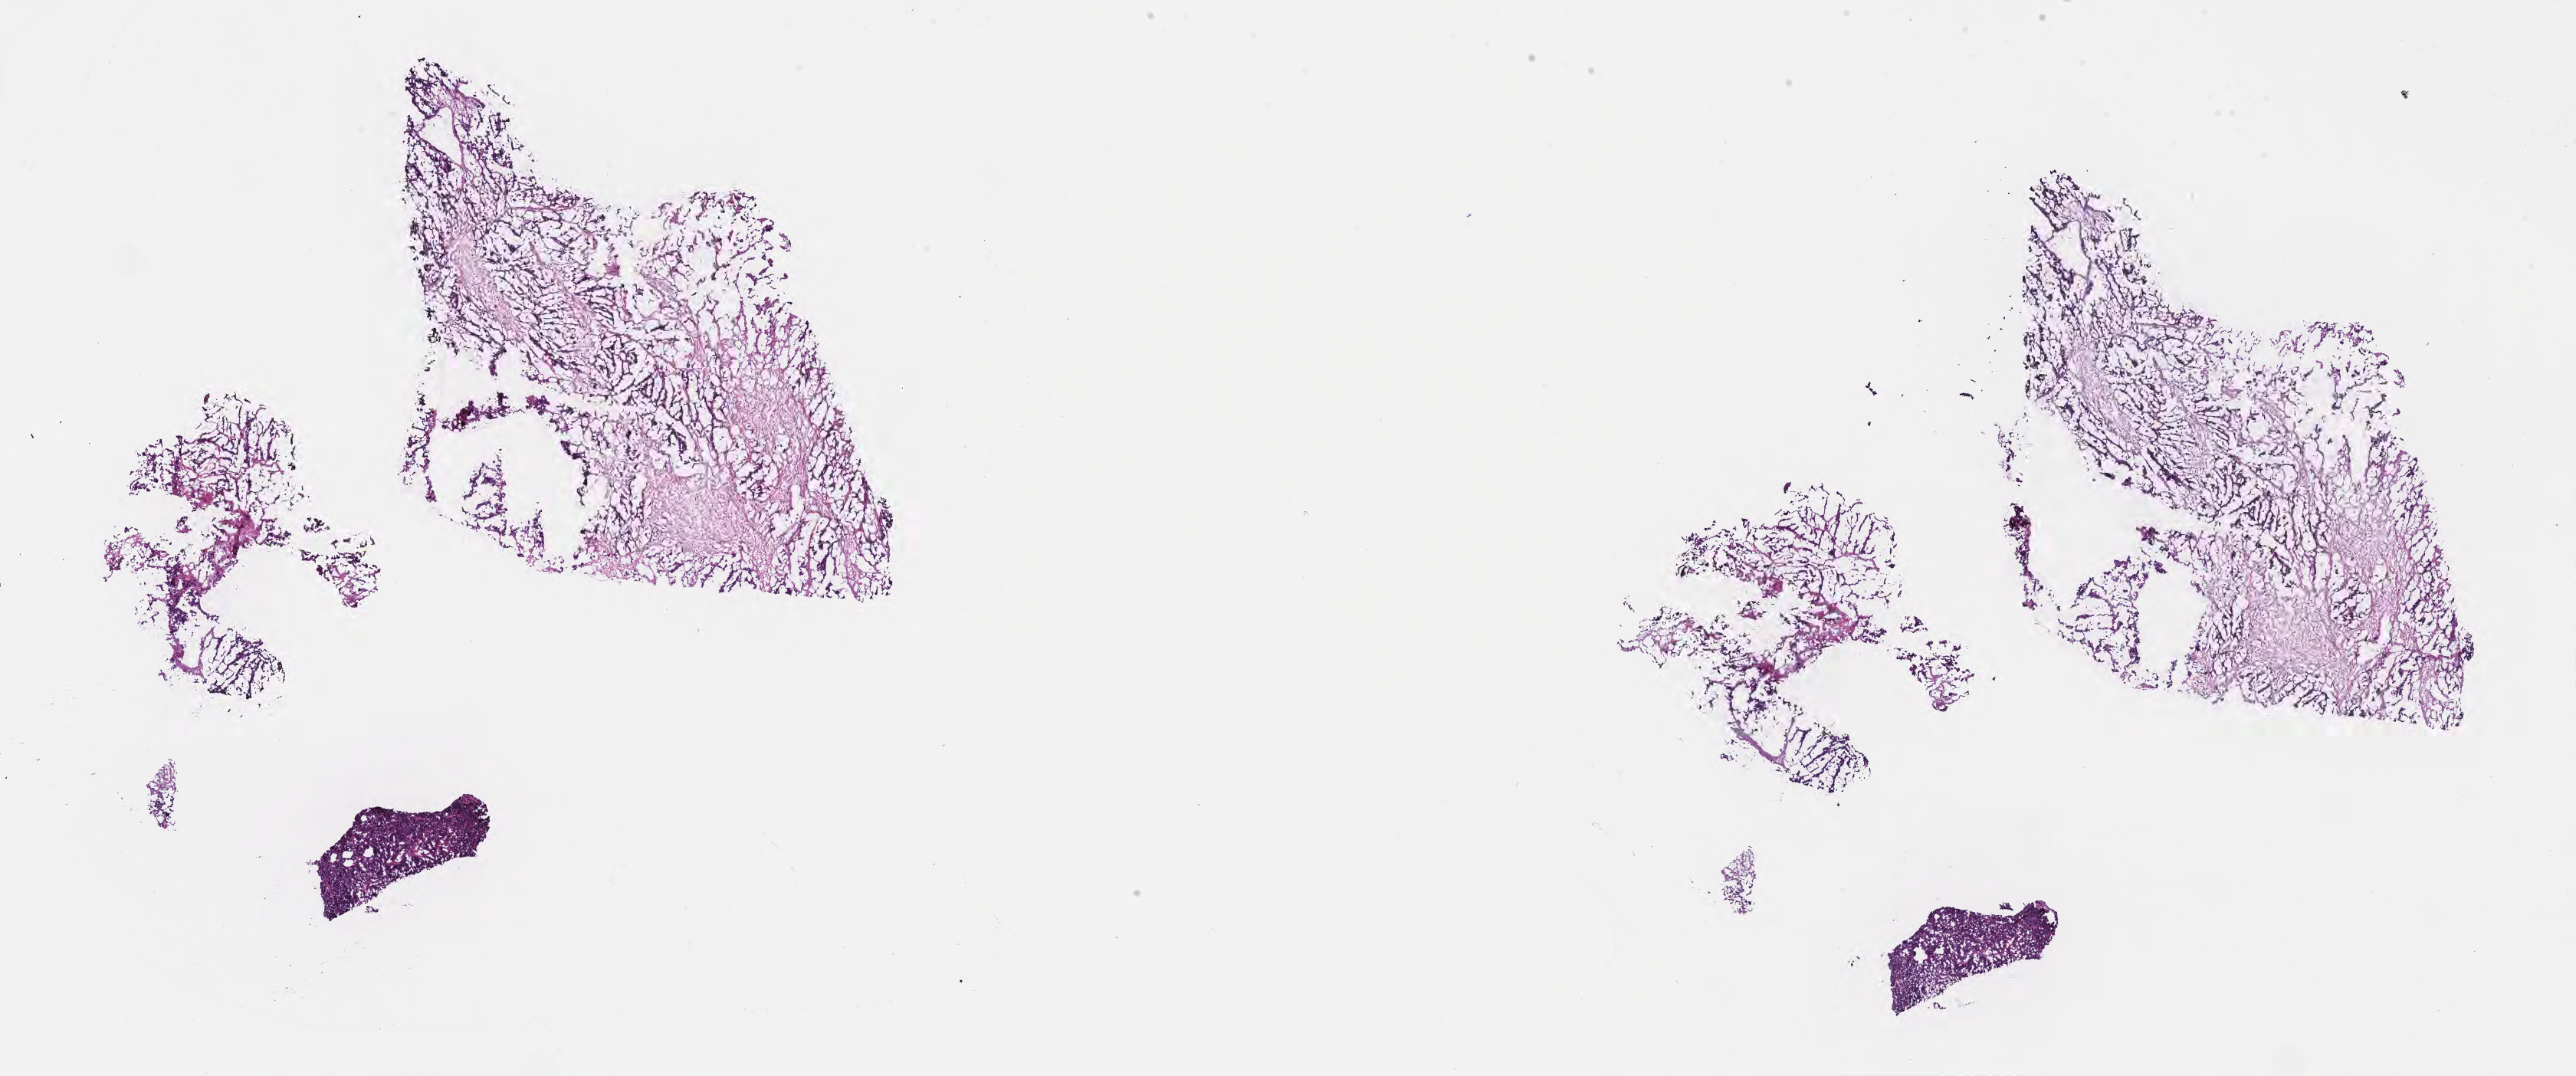
Digitized H&E-stained section — whole scanned area (about 27.2 x 11.4 mm) shown as a low-resolution overview, cryosection, specimen: metastatic tumor tissue, resected from pleura. Male patient; age at initial diagnosis 12 years. Slide review estimates, as recorded: tumor cells 100%, tumor nuclei 70%, stromal cells 0%, necrosis 0%, normal cells 0%. Inflammatory infiltration, as recorded: lymphocyte infiltration 0%, monocyte infiltration 0%, neutrophil infiltration 0%.
Section: top of the tissue portion. Patient diagnosis (primary): Mixed type rhabdomyosarcoma.